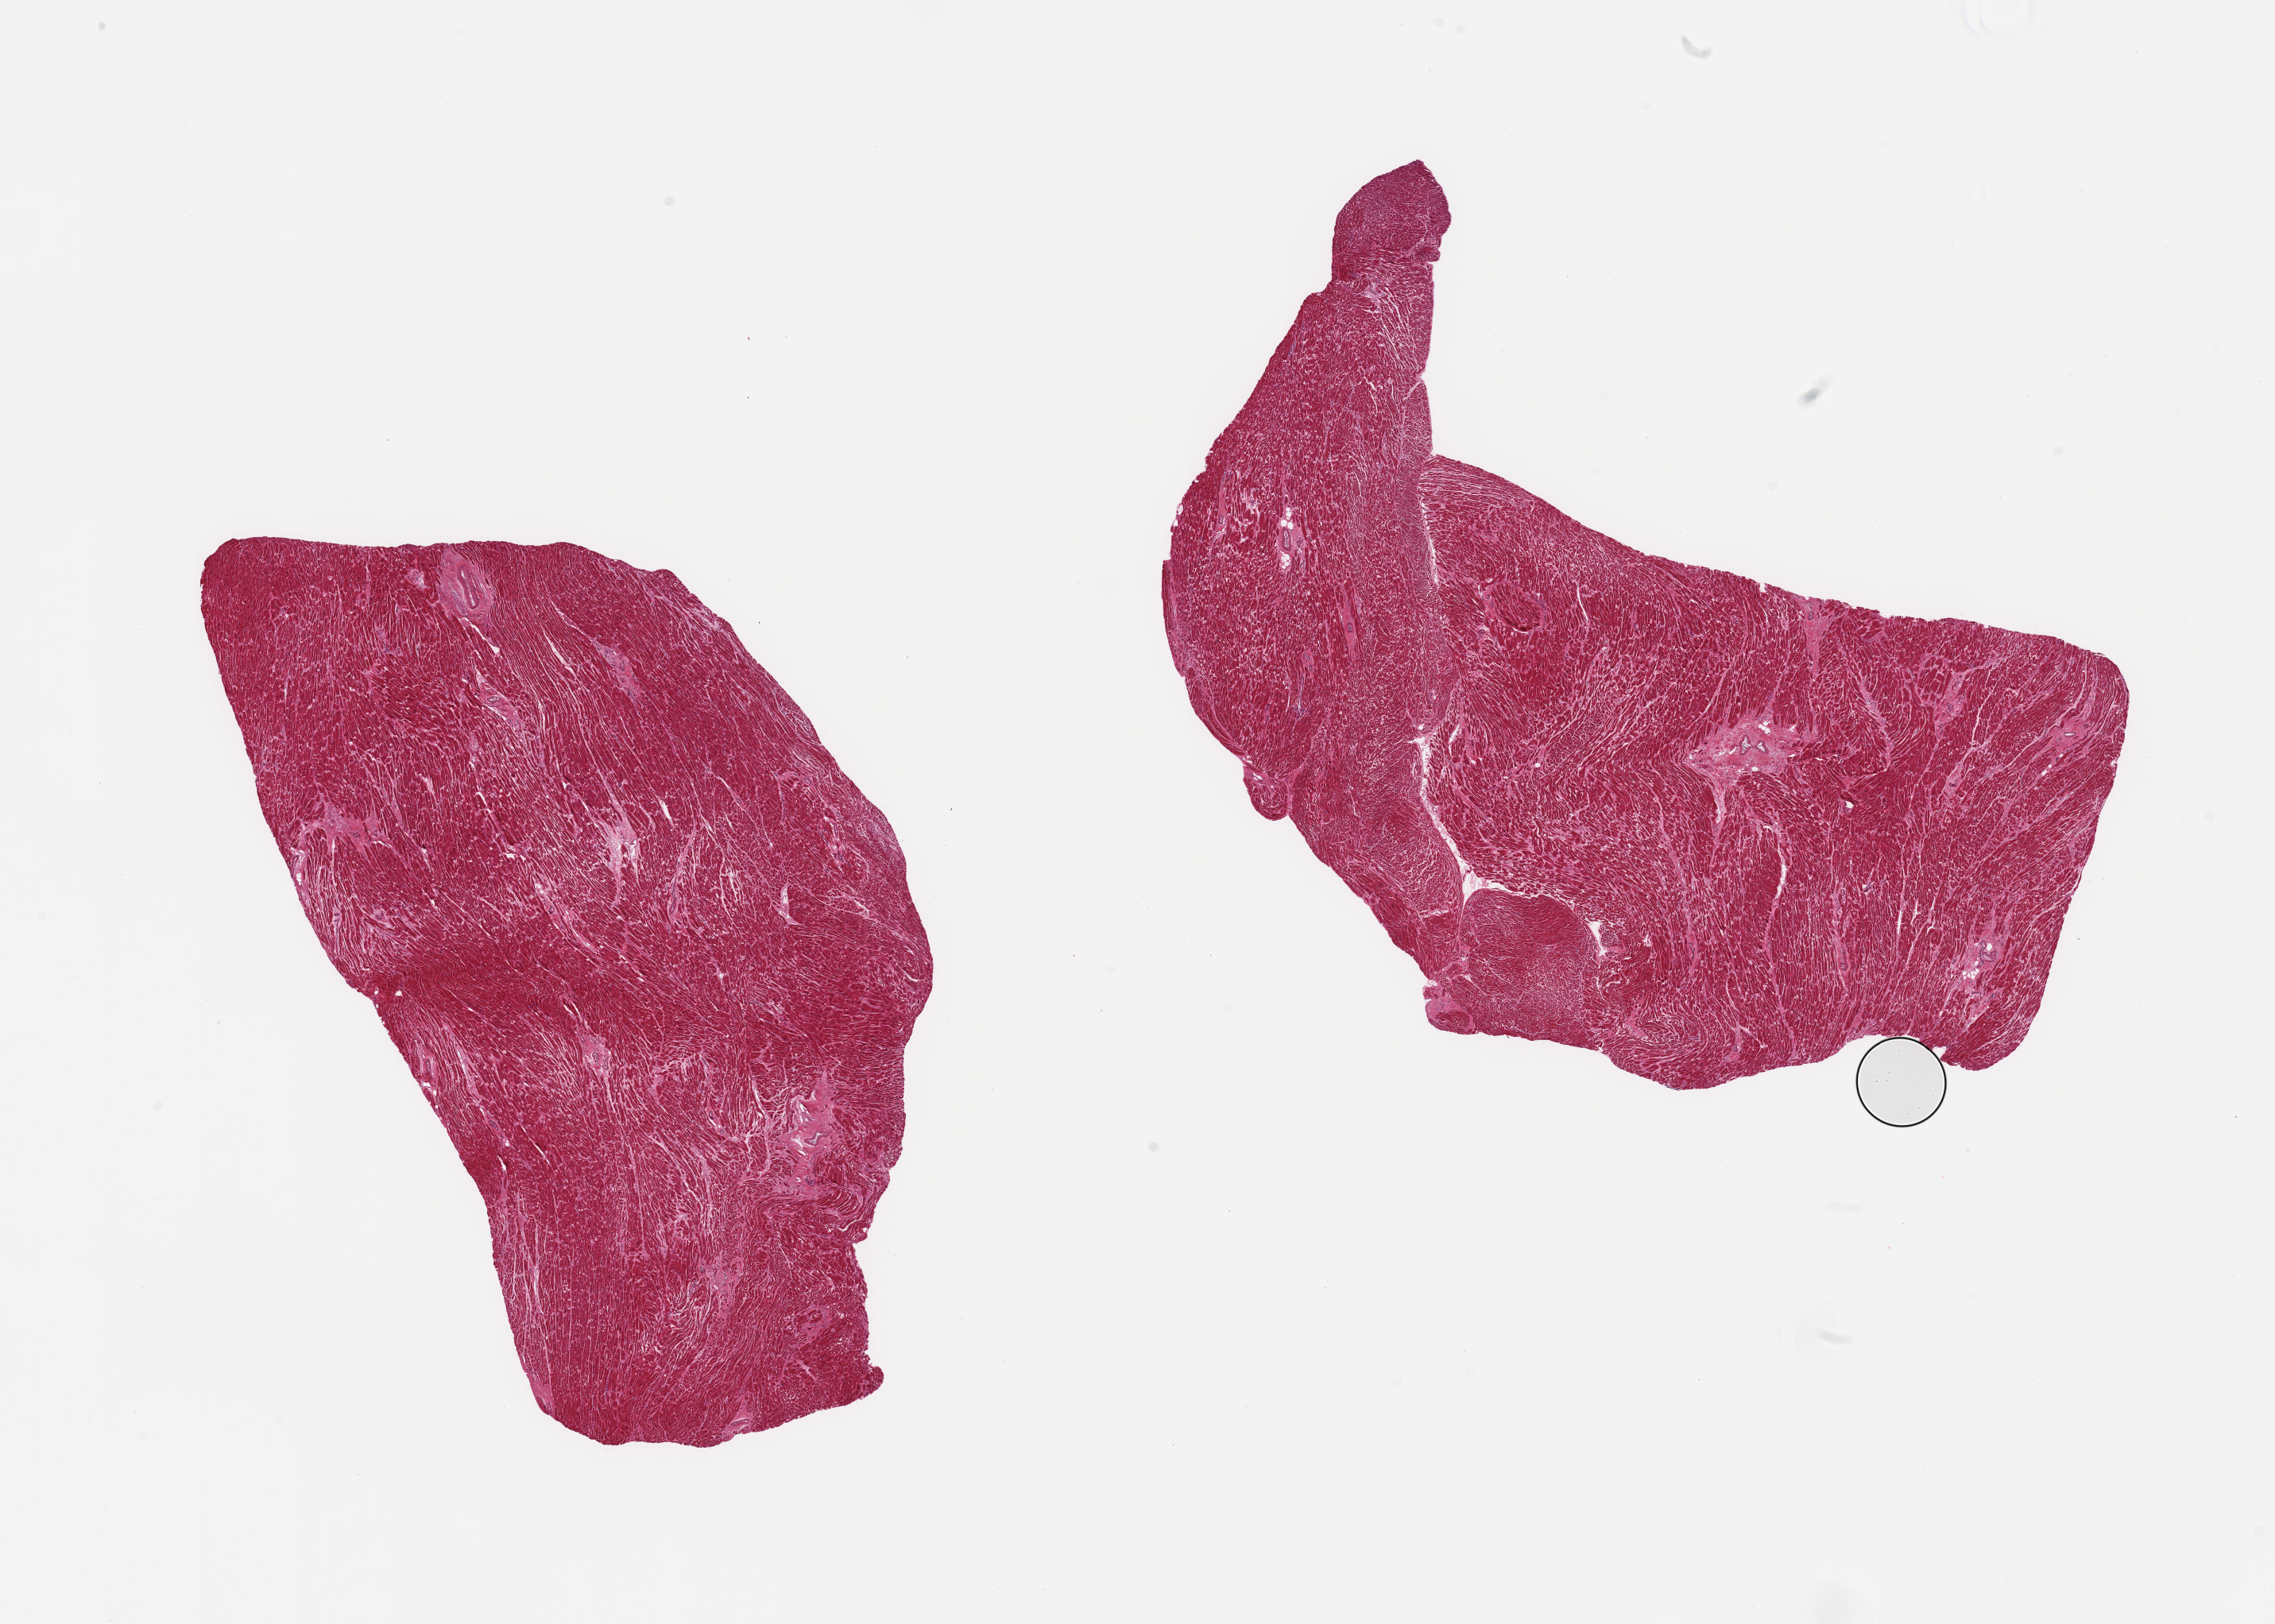
Digitized haematoxylin and eosin-stained section — shown as a low-resolution overview of the whole scanned area (about 22.6 x 16.2 mm), PAXgene-fixed, paraffin-embedded tissue, target tissue: heart, tissue donor sample. Male donor.
Pathologist's review note for this sample: 2 pieces, moderate-marked chronic ischemic changes/interstitial fibrosis.